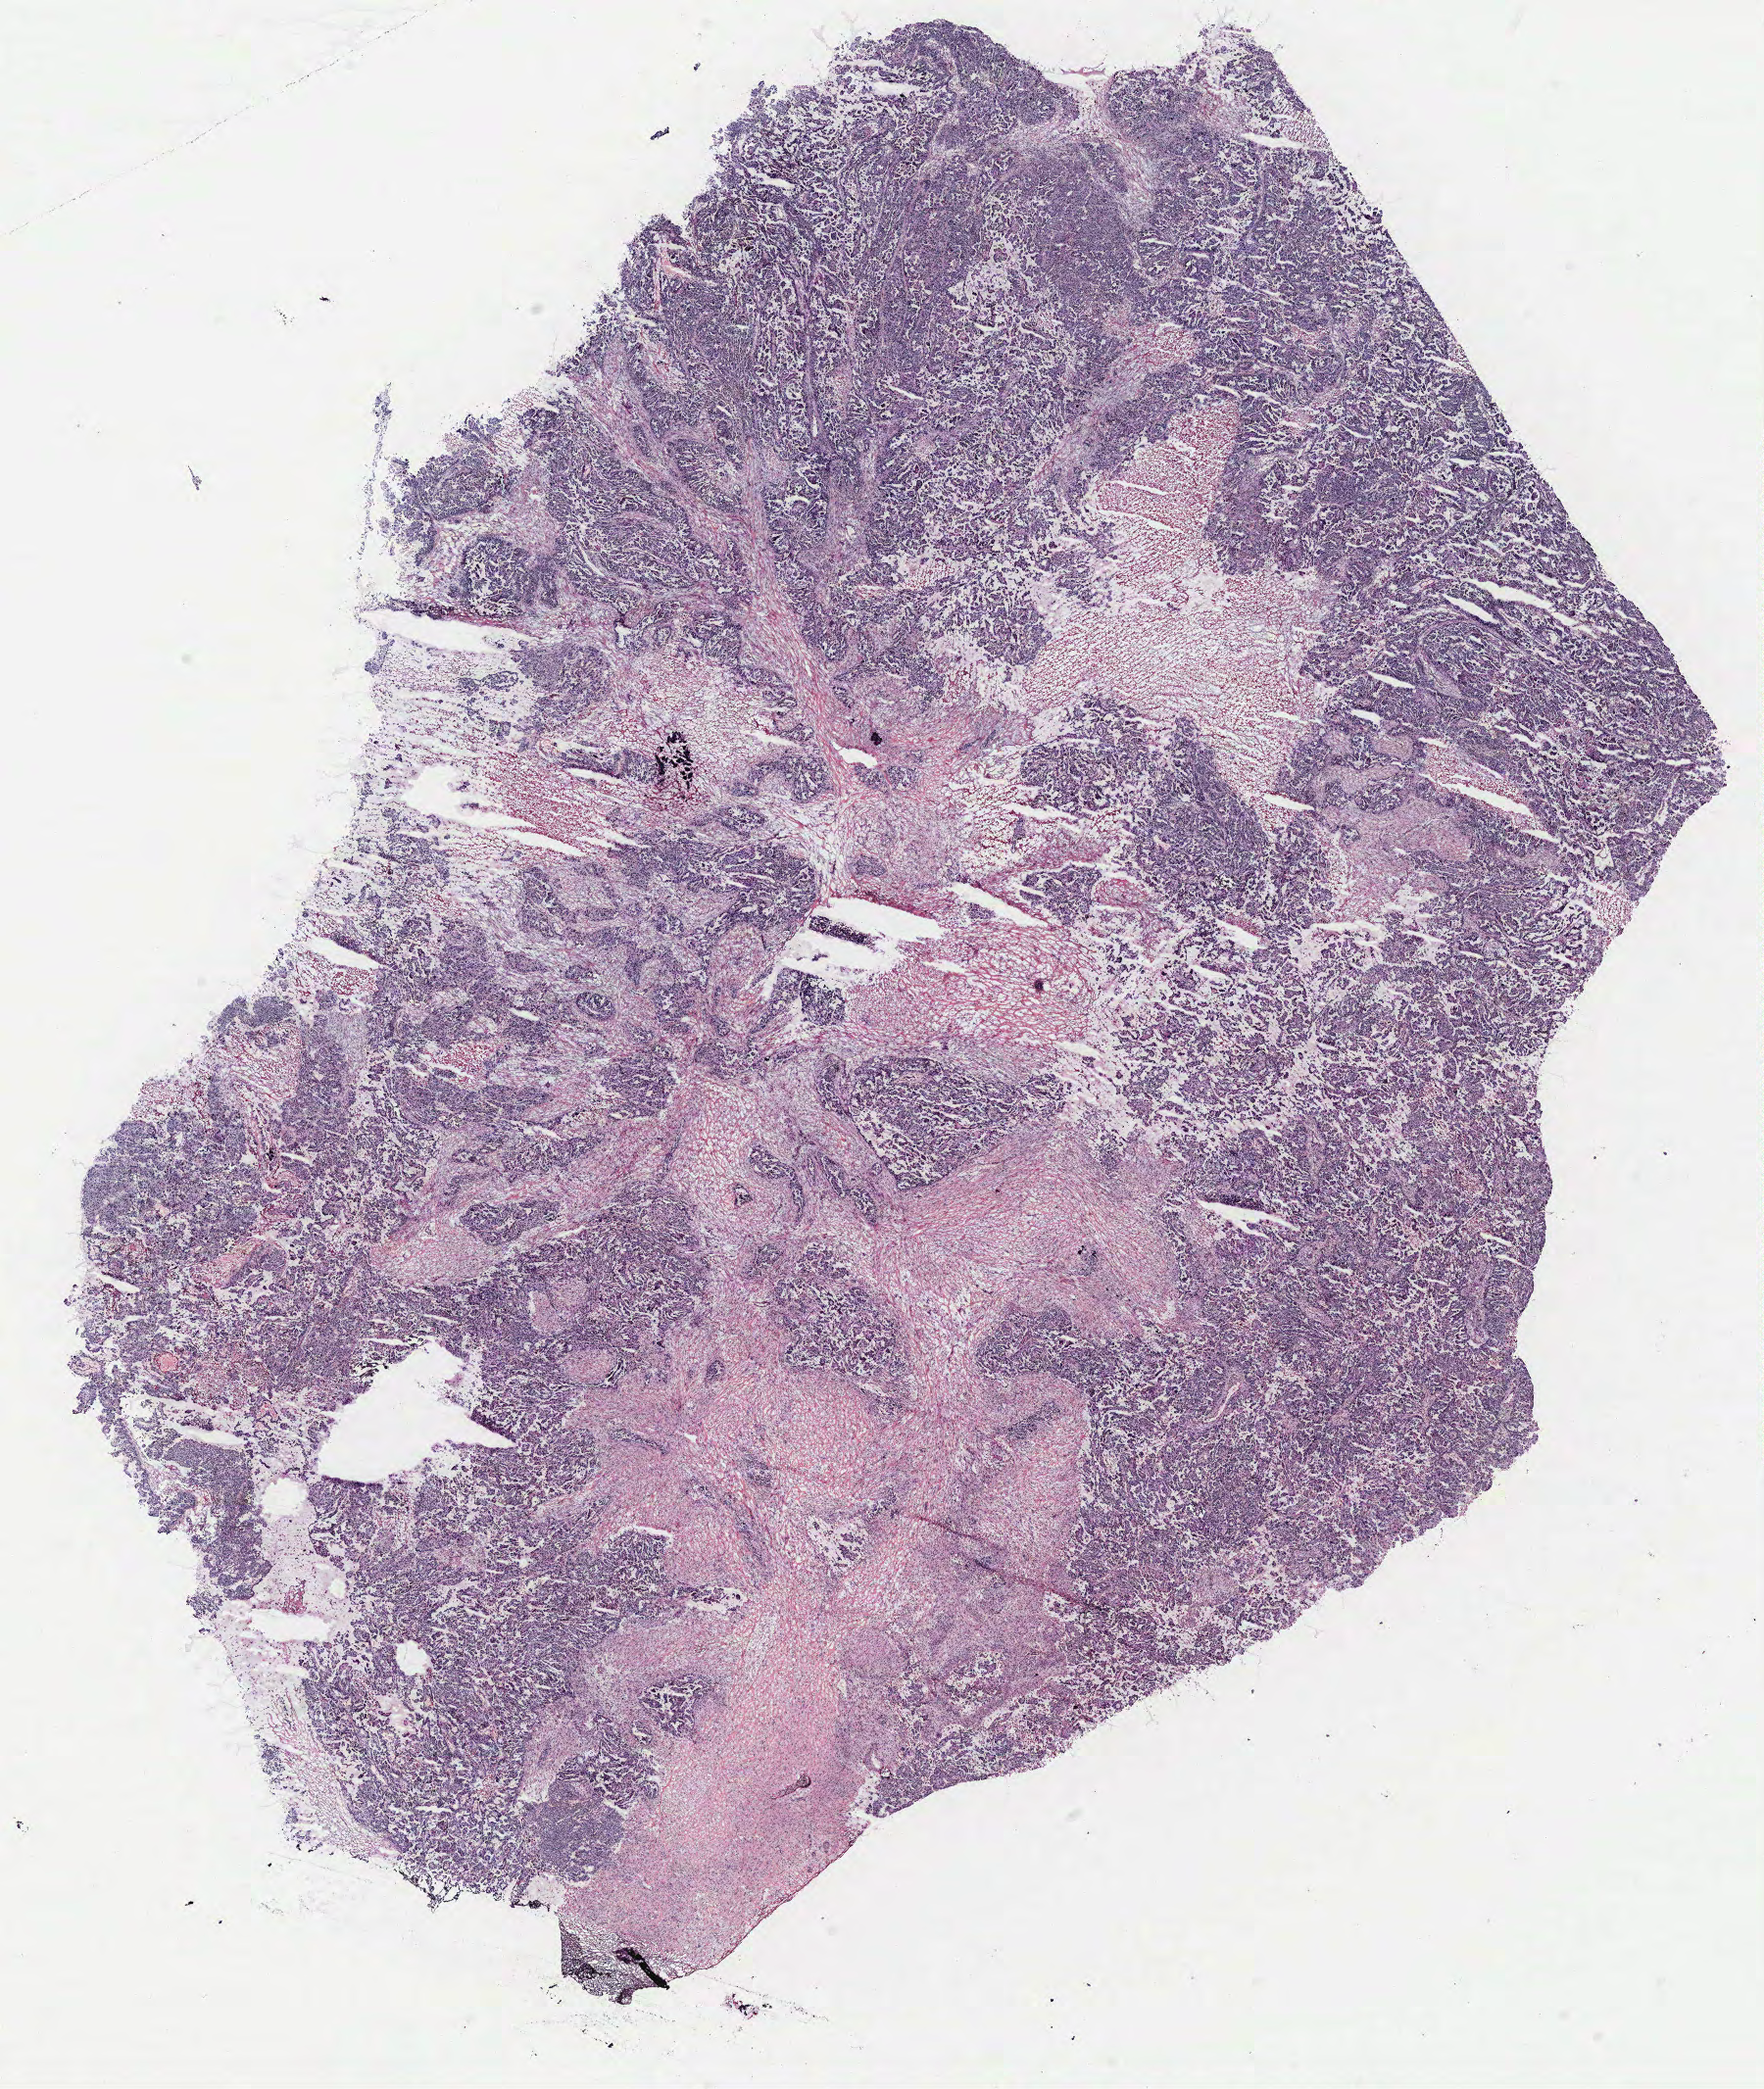
H&E-stained whole-slide image — a low-resolution overview of the entire scanned area, about 14.4 x 17.1 mm (slide scanned at 40x). Tumour tissue sample, ovary. Patient: female, age 56 years.
Histologic diagnosis: Serous adenocarcinoma, NOS. Primary tumour site (as recorded): ovary.